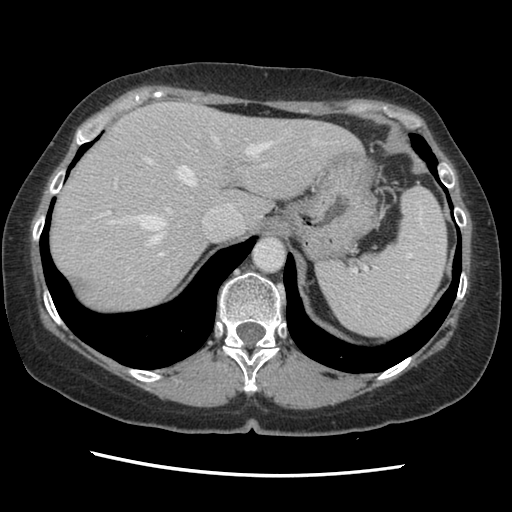
Contrast-enhanced abdominal CT, one axial slice; slice 105 of 141 in the series (ordered by position); soft-tissue window (W 400 / L 40 HU); 2.5 mm slice thickness; 512 × 512 image matrix. Female patient, age 61 years. Case-level facts recorded for this patient, not image findings: diagnosis: colorectal cancer liver metastases, imaged before liver resection; multiple liver metastases: no; largest metastasis: 2.4 cm; disease in both lobes: no.
Annotated regions visible in this slice (outlined manually by an expert reader):
- hepatic veins: box from (x=82, y=130) to (x=316, y=245) px
- liver: (x=51, y=102)–(x=359, y=315)
- planned liver remnant (the part of the liver to remain after resection): (x=51, y=102)–(x=359, y=315)
- portal vein (with intrahepatic branches): (x=100, y=150)–(x=270, y=257)